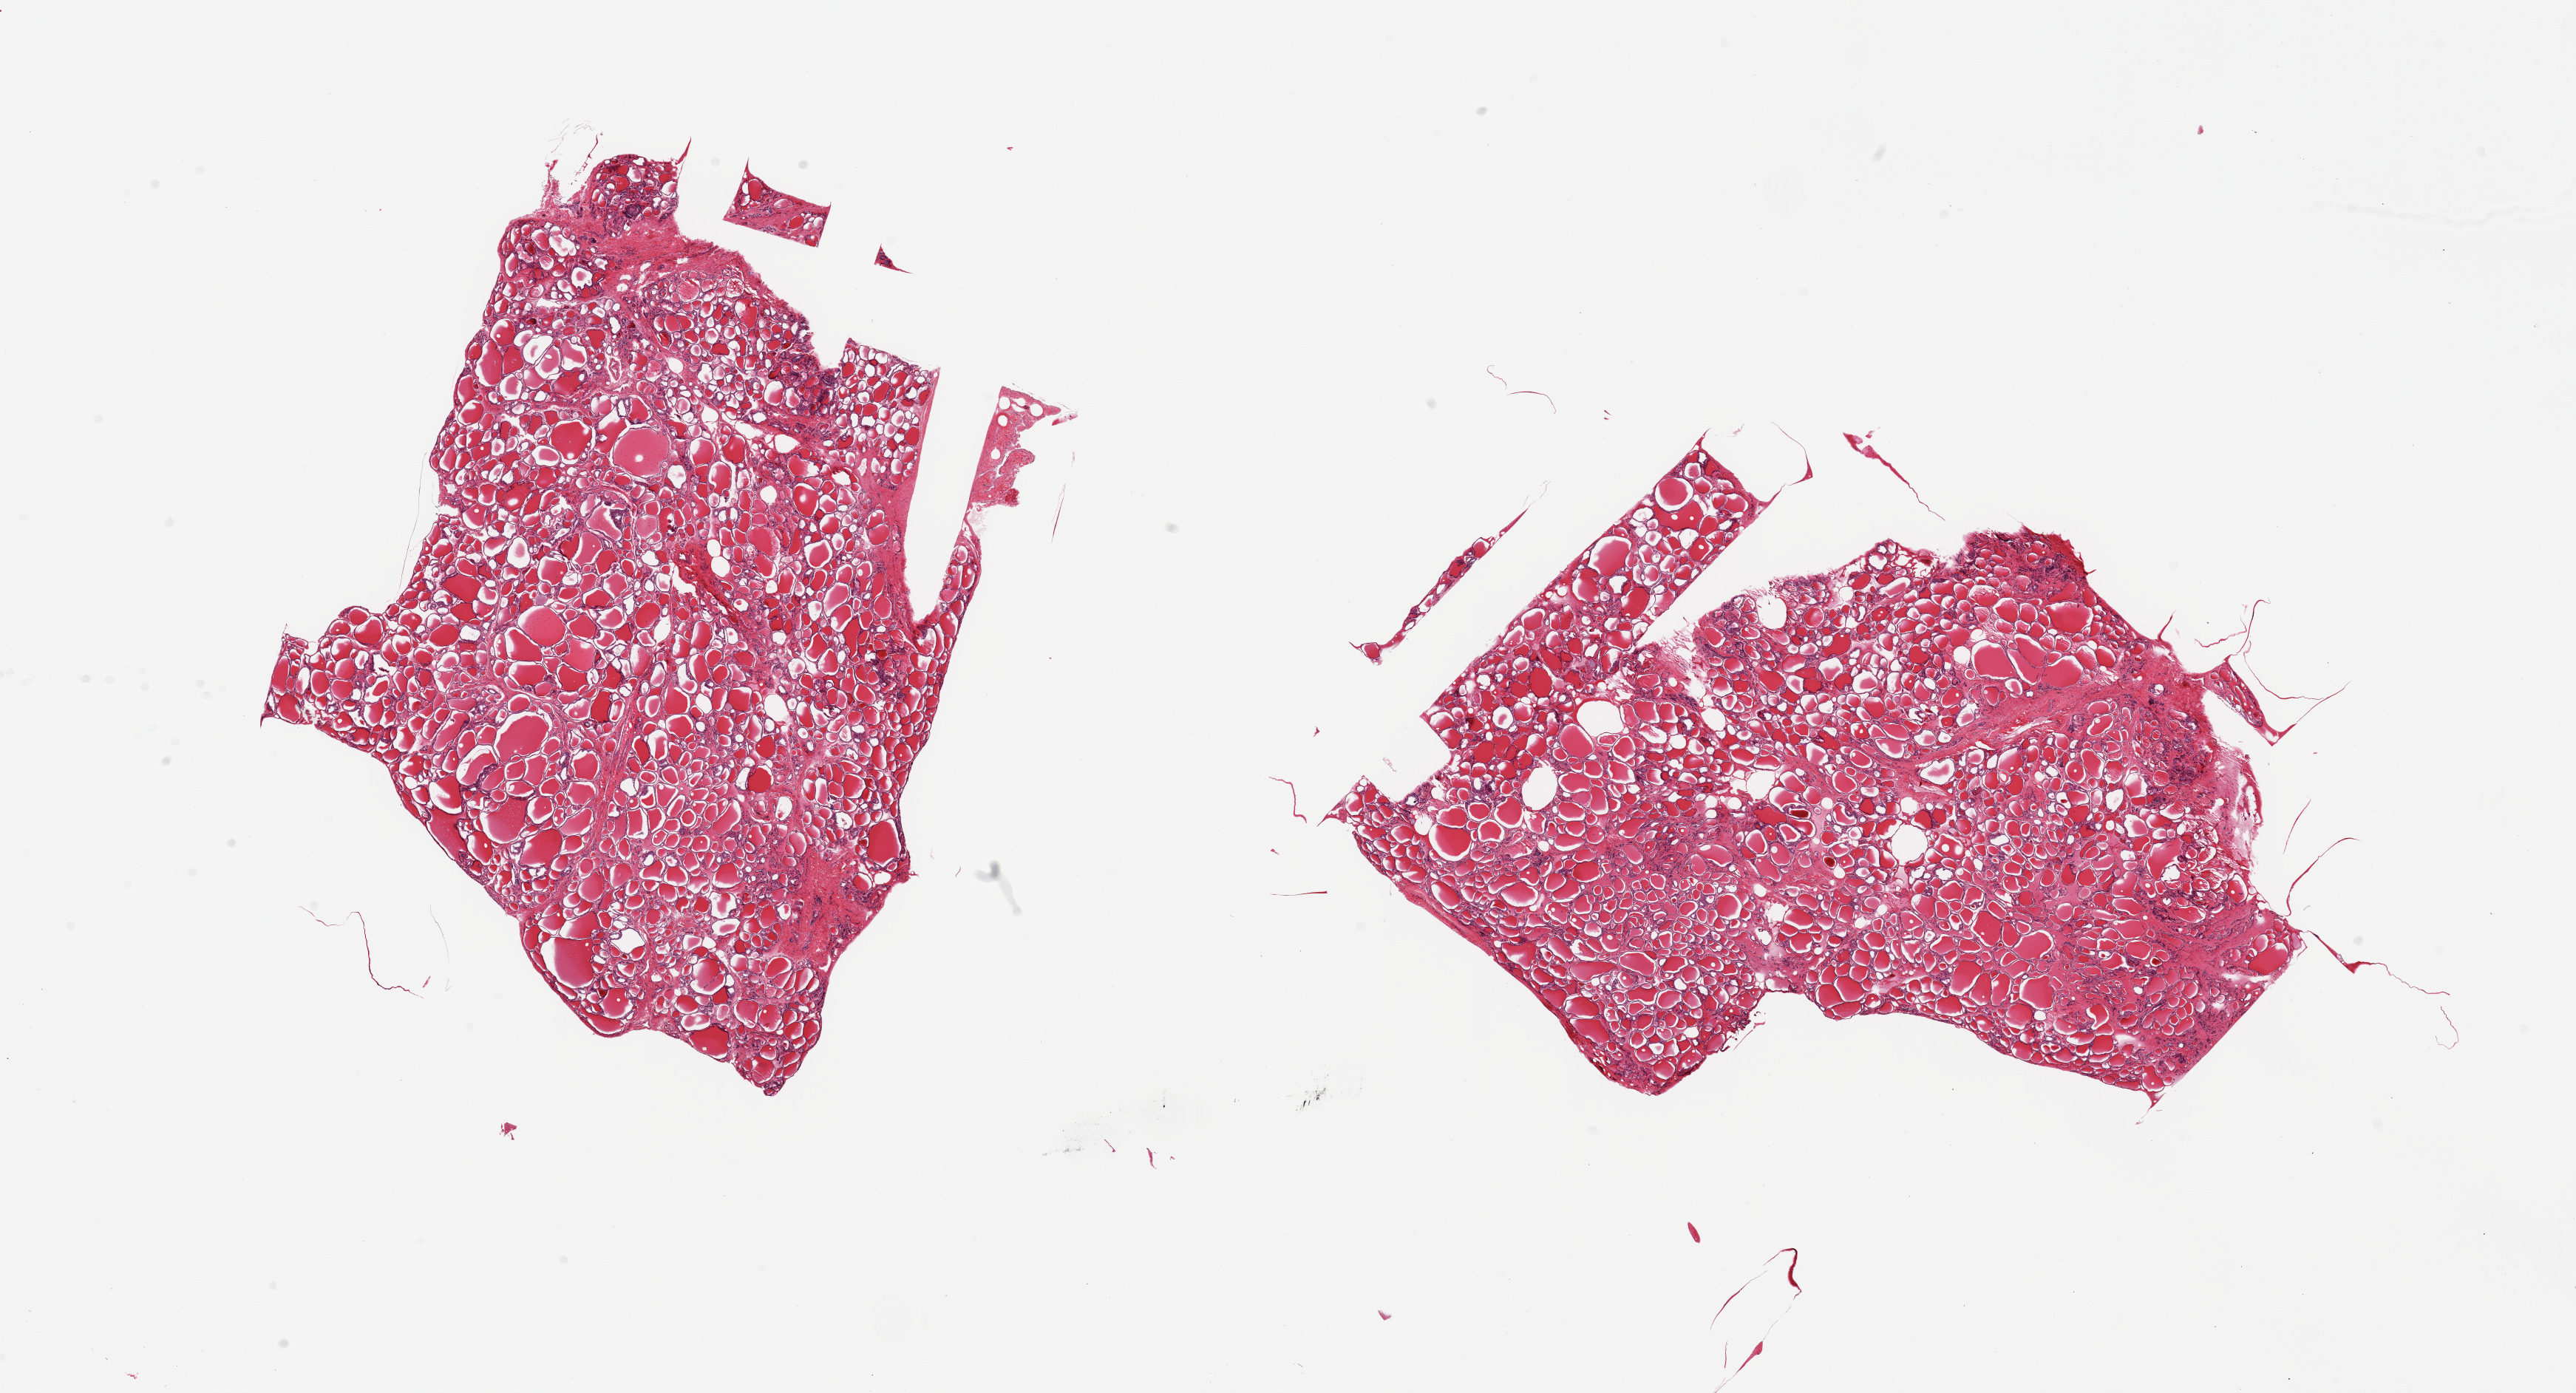
Digitized H&E-stained section, a low-resolution overview of the entire scanned area, about 27.6 x 14.9 mm, PAXgene-fixed, paraffin-embedded tissue, sampled site (target tissue): thyroid, donor tissue sample. Donor sex: female.
Review note (as recorded): 2 pieces.